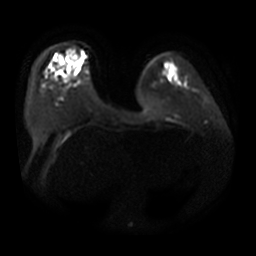
Breast MRI, one axial slice; position 9 of 31 along the scan axis; diffusion-weighted series; image 2 of 4 stored at this slice position (different b-values; order by instance number); 3 T; 5 mm slice thickness; 256 × 256 image matrix, field of view 380 × 380 mm. Female patient.
Annotated regions visible in this slice (expert manual segmentation):
- tumour on diffusion-weighted imaging: bounding box <68,59,77,65> (left, top, right, bottom; pixels)